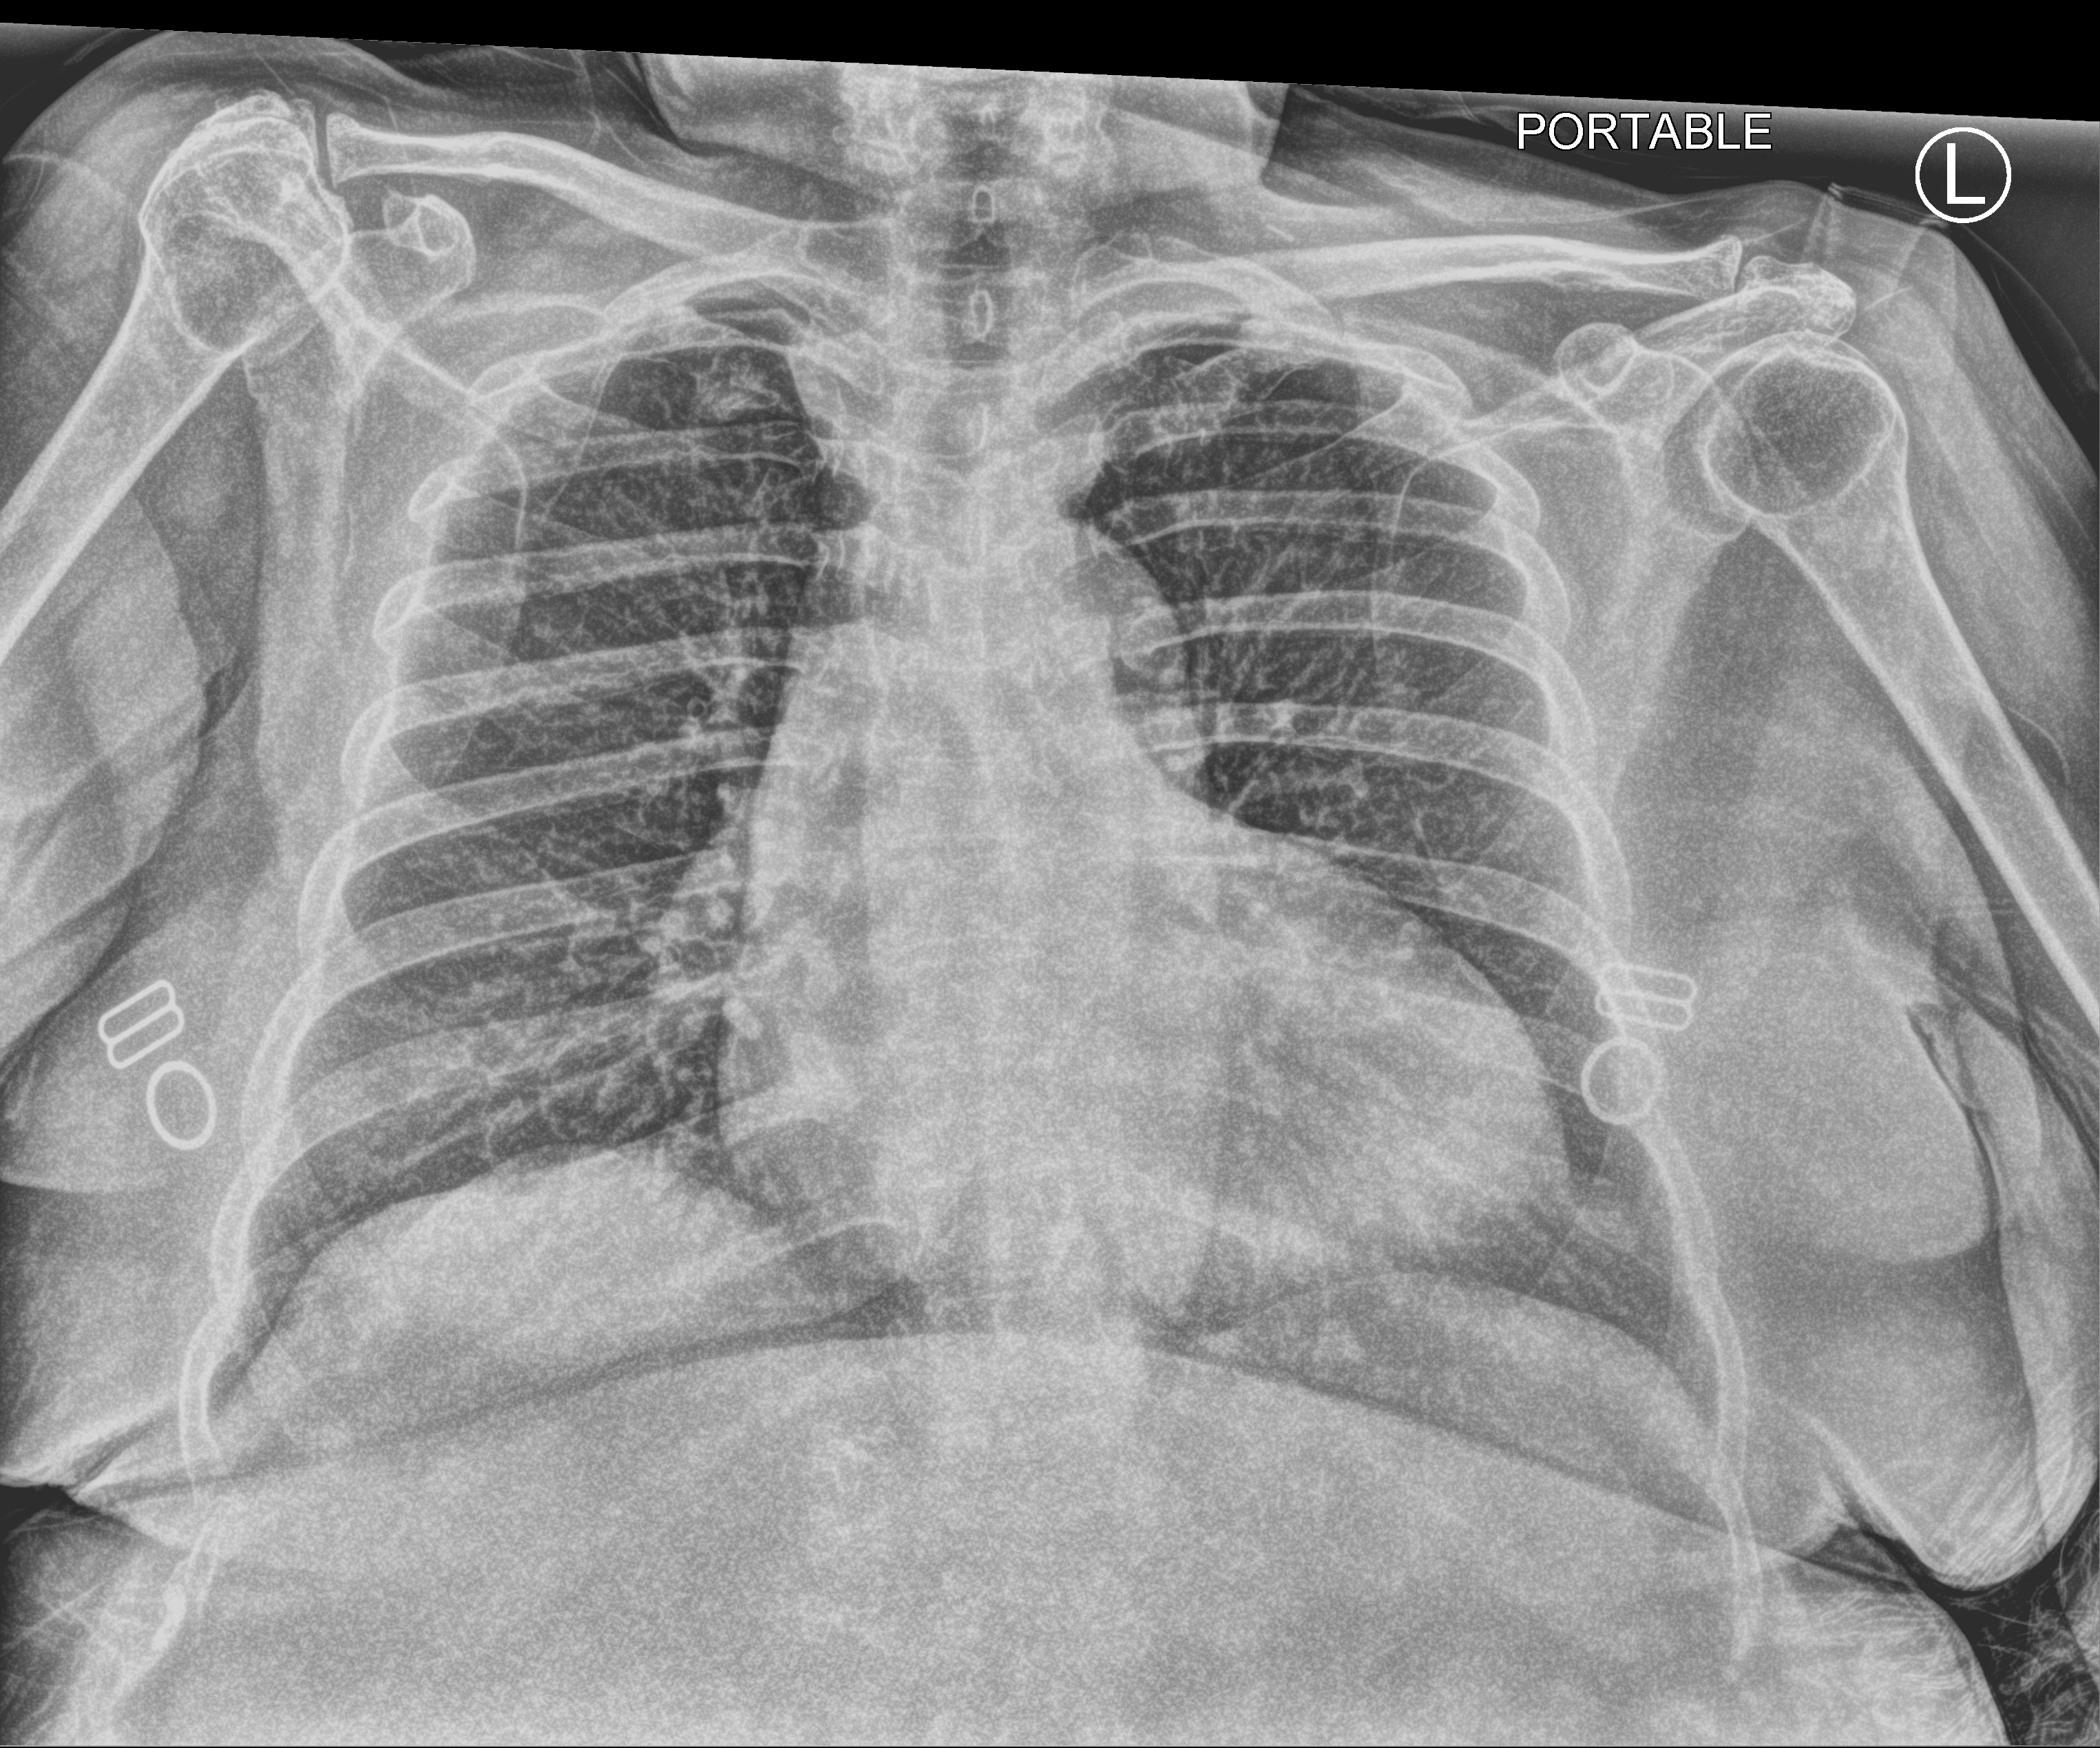
Bedside chest radiograph (computed radiography), anteroposterior (AP) projection. Patient hospitalised with COVID-19; female, aged 75–90 years.
Hospital-stay facts (about this admission, not read from this image; timing relative to this image not recorded): admitted to intensive care during this hospital stay: no; mechanically ventilated during this hospital stay: no.